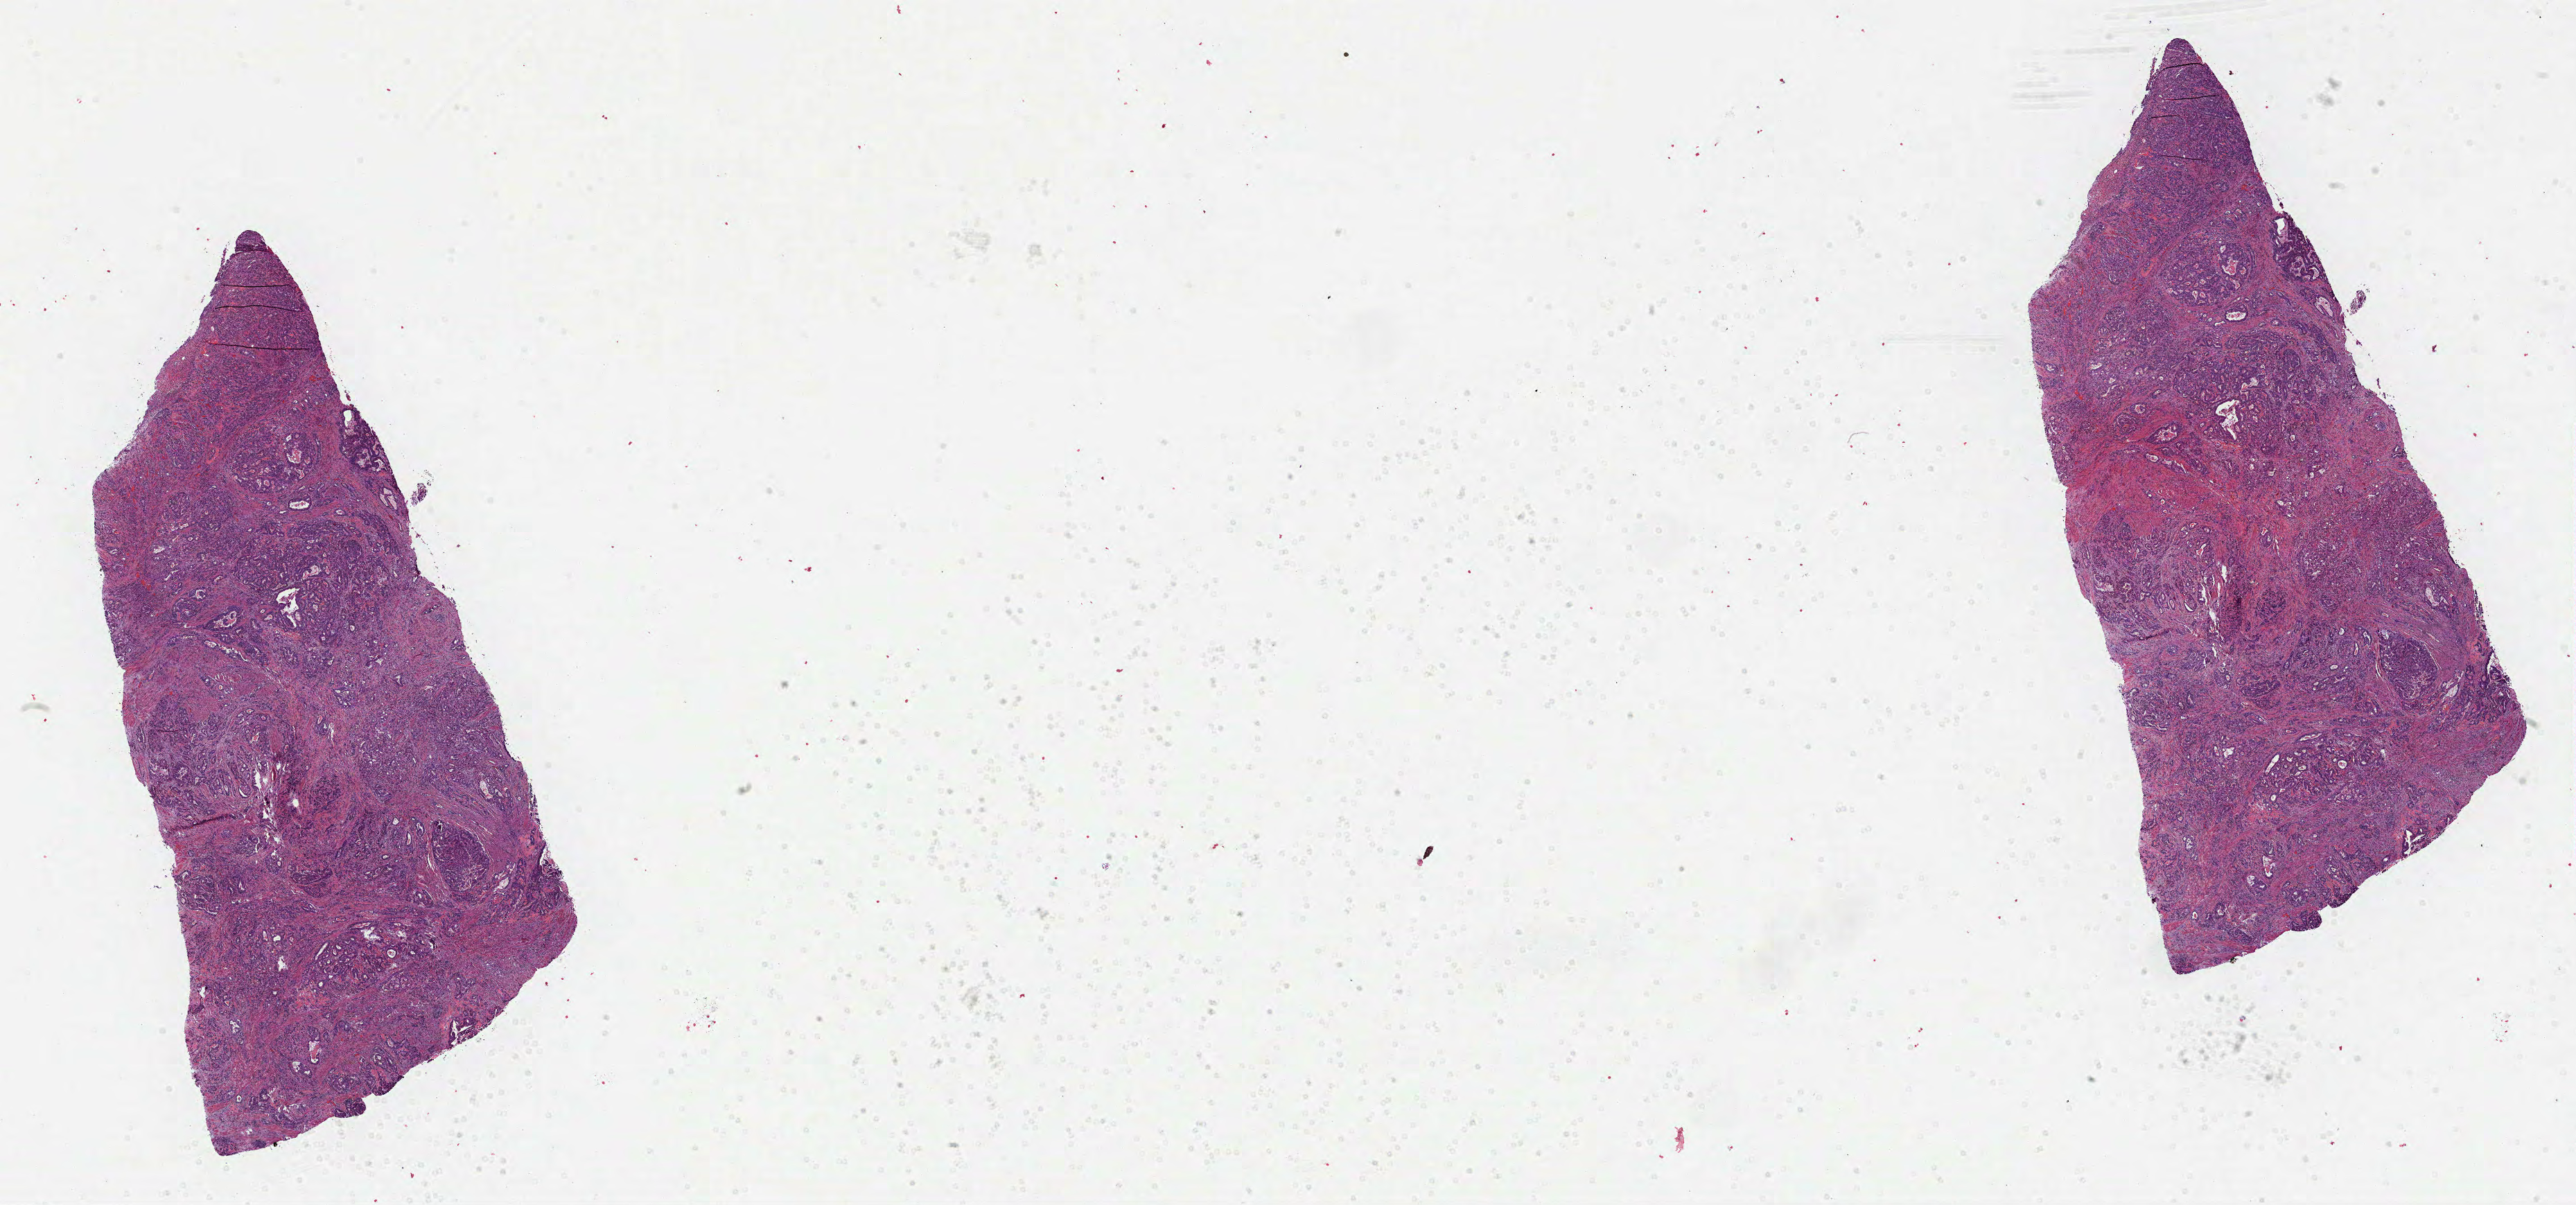
Whole-slide histology image, H&E-stained, low-resolution overview of the scanned area, about 30.0 x 14.0 mm. Formalin-fixed paraffin-embedded (FFPE) diagnostic section. Primary tumour sample from the stomach. Patient: female, age at initial diagnosis 86 years. Histologic grade: G2 (moderately differentiated).
Lymph nodes positive (case pathology): 8 of 10 examined. AJCC pathologic stage: IV (7th edition). Pathologic diagnosis: Adenocarcinoma, NOS (gastric antrum).